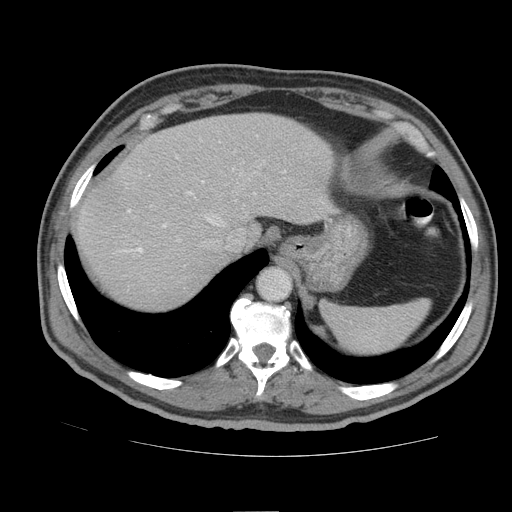
Contrast-enhanced abdominal CT (liver protocol), one axial slice; position 70 of 105 along the scan axis; reconstruction kernel STANDARD; 140 kVp; soft-tissue window (W 400 / L 40 HU); 512 × 512 image matrix, field of view 380 × 380 mm. Case-level facts recorded for this patient, not image findings: diagnosis: hepatocellular carcinoma (patient treated with transarterial chemoembolisation; whether this scan precedes or follows treatment is not stated here); TNM stage (as recorded): Stage-IIIB; Child-Pugh class: A; tumour nodularity: multinodular.
Outlined on this slice (semi-automatic segmentation, software-assisted and operator-edited):
- abdominal aorta: box from (x=259, y=269) to (x=289, y=298) px
- liver parenchyma outside the tumour (the mass and vessels are separate outlines, so this box may not span the whole liver): (x=76, y=112)–(x=334, y=308)
- liver vessels: (x=121, y=171)–(x=285, y=253)